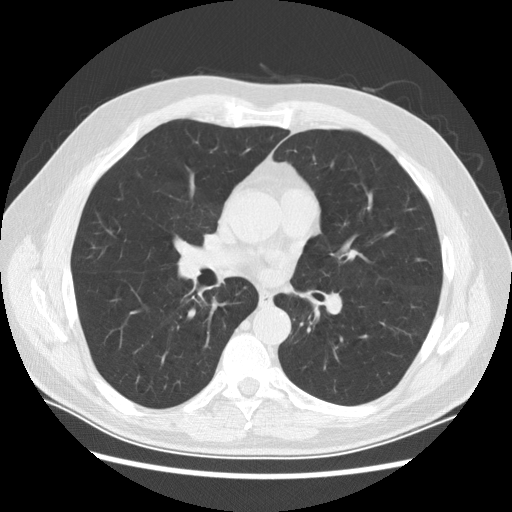
Low-dose screening chest CT, axial slice. Baseline screening round. Lung window (W 1500 / L -600 HU). 2.5 mm slice thickness. Standard (soft-tissue) reconstruction kernel (STANDARD). Slice 117 of 241 in the series. 512 × 512 image matrix. Male, age 61 years at enrolment.
- Lesion marked by an expert reader, bounding box (x1, y1, x2, y2) in pixels: (225, 278, 252, 312).
- No non-calcified nodule or mass ≥4 mm was recorded by the screening reader at this exam.
- Participant outcome: lung cancer diagnosed 756 days after this screen (after the third annual screen) — squamous cell carcinoma, keratinizing, NOS, right lower lobe, stage IIIB (AJCC 6th edition), 40 mm at pathology.